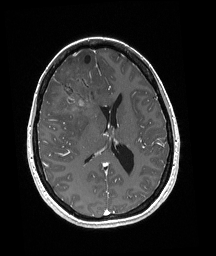
Brain MRI from a brain-tumour surgery series, one axial slice. Slice 87 of 192 in the series (ordered by position). T1-weighted post-contrast. 1 mm slice thickness. 216 × 256 image matrix. Case-level facts recorded for this patient, not image findings: histopathology: Oligodendroglioma; WHO grade: 3; IDH mutation: yes; tumour location: Right Frontal.
Outlined on this slice (manually delineated by an expert):
- tumour: bounding box (x1, y1, x2, y2) in pixels: (53, 67, 102, 117)